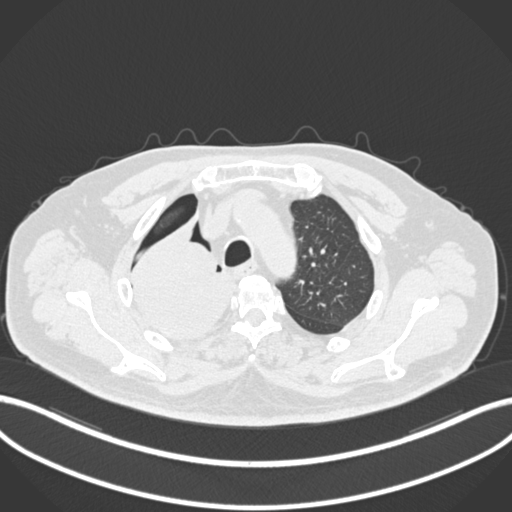
Chest CT, one axial slice. Slice 167 of 218 in the series (ordered by position). Reconstruction kernel B30f. 120 kVp. Lung window (W 1500 / L -600 HU). 1 mm slice thickness. 512 × 512 image matrix. Male patient, age 68 years. From the clinical record (not read from this slice): clinical TNM (as recorded): T2a N0 M0.
Annotated regions visible in this slice (bounding box drawn by a radiologist):
- lung tumour (recorded histology: adenocarcinoma): bounding box <132,229,229,338> (left, top, right, bottom; pixels)